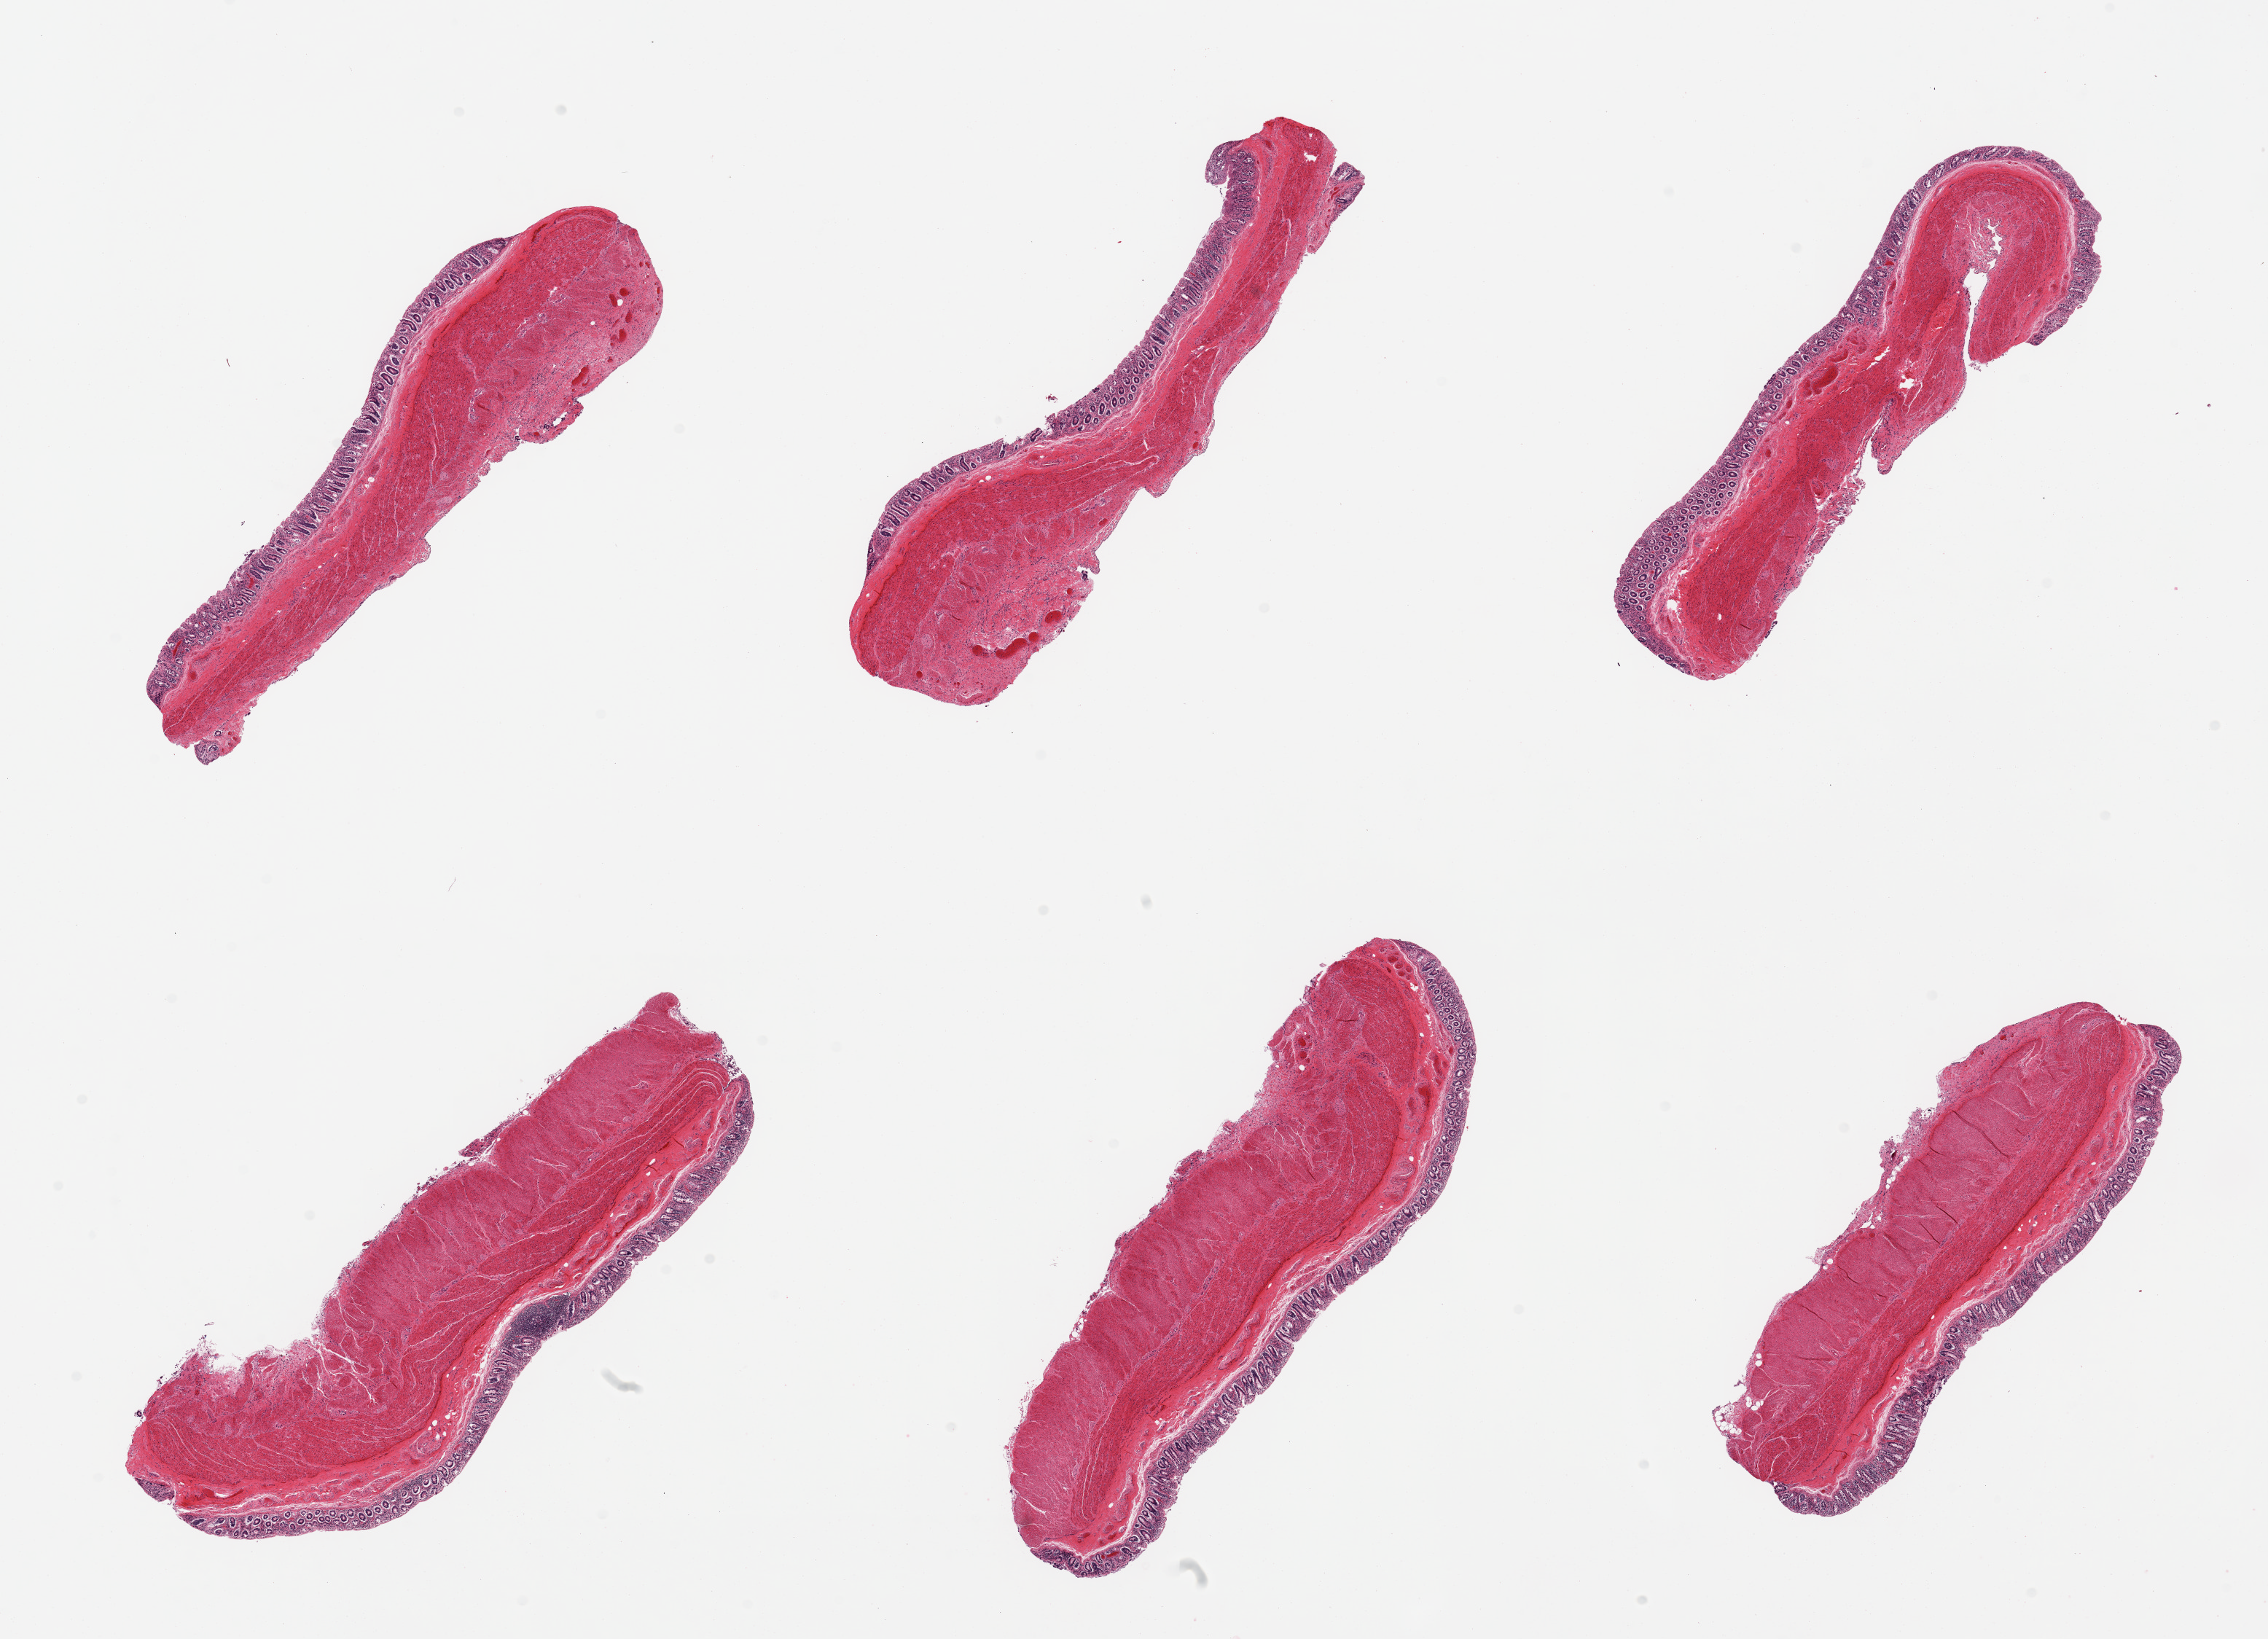
Haematoxylin and eosin whole-slide image — low-resolution overview of the scanned area, about 24.6 x 17.8 mm (acquisition: 20x scan). PAXgene-fixed paraffin-embedded (PFPE) section. Section of transverse colon (target tissue). Tissue donor sample. Donor: male.
* pathologist's review note for this sample: 6 pieces, glandular component of mucosa markedly autolyzed, up to~0.3mm, ~15% thickness